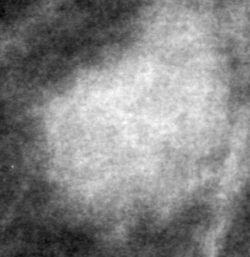
Crop from a digitized film mammogram around one marked abnormality; left breast; MLO view; BI-RADS breast density category 2 (scale 1–4).
- Mass, shape lobulated, margins obscured; BI-RADS assessment category 4; pathology (as recorded): benign.